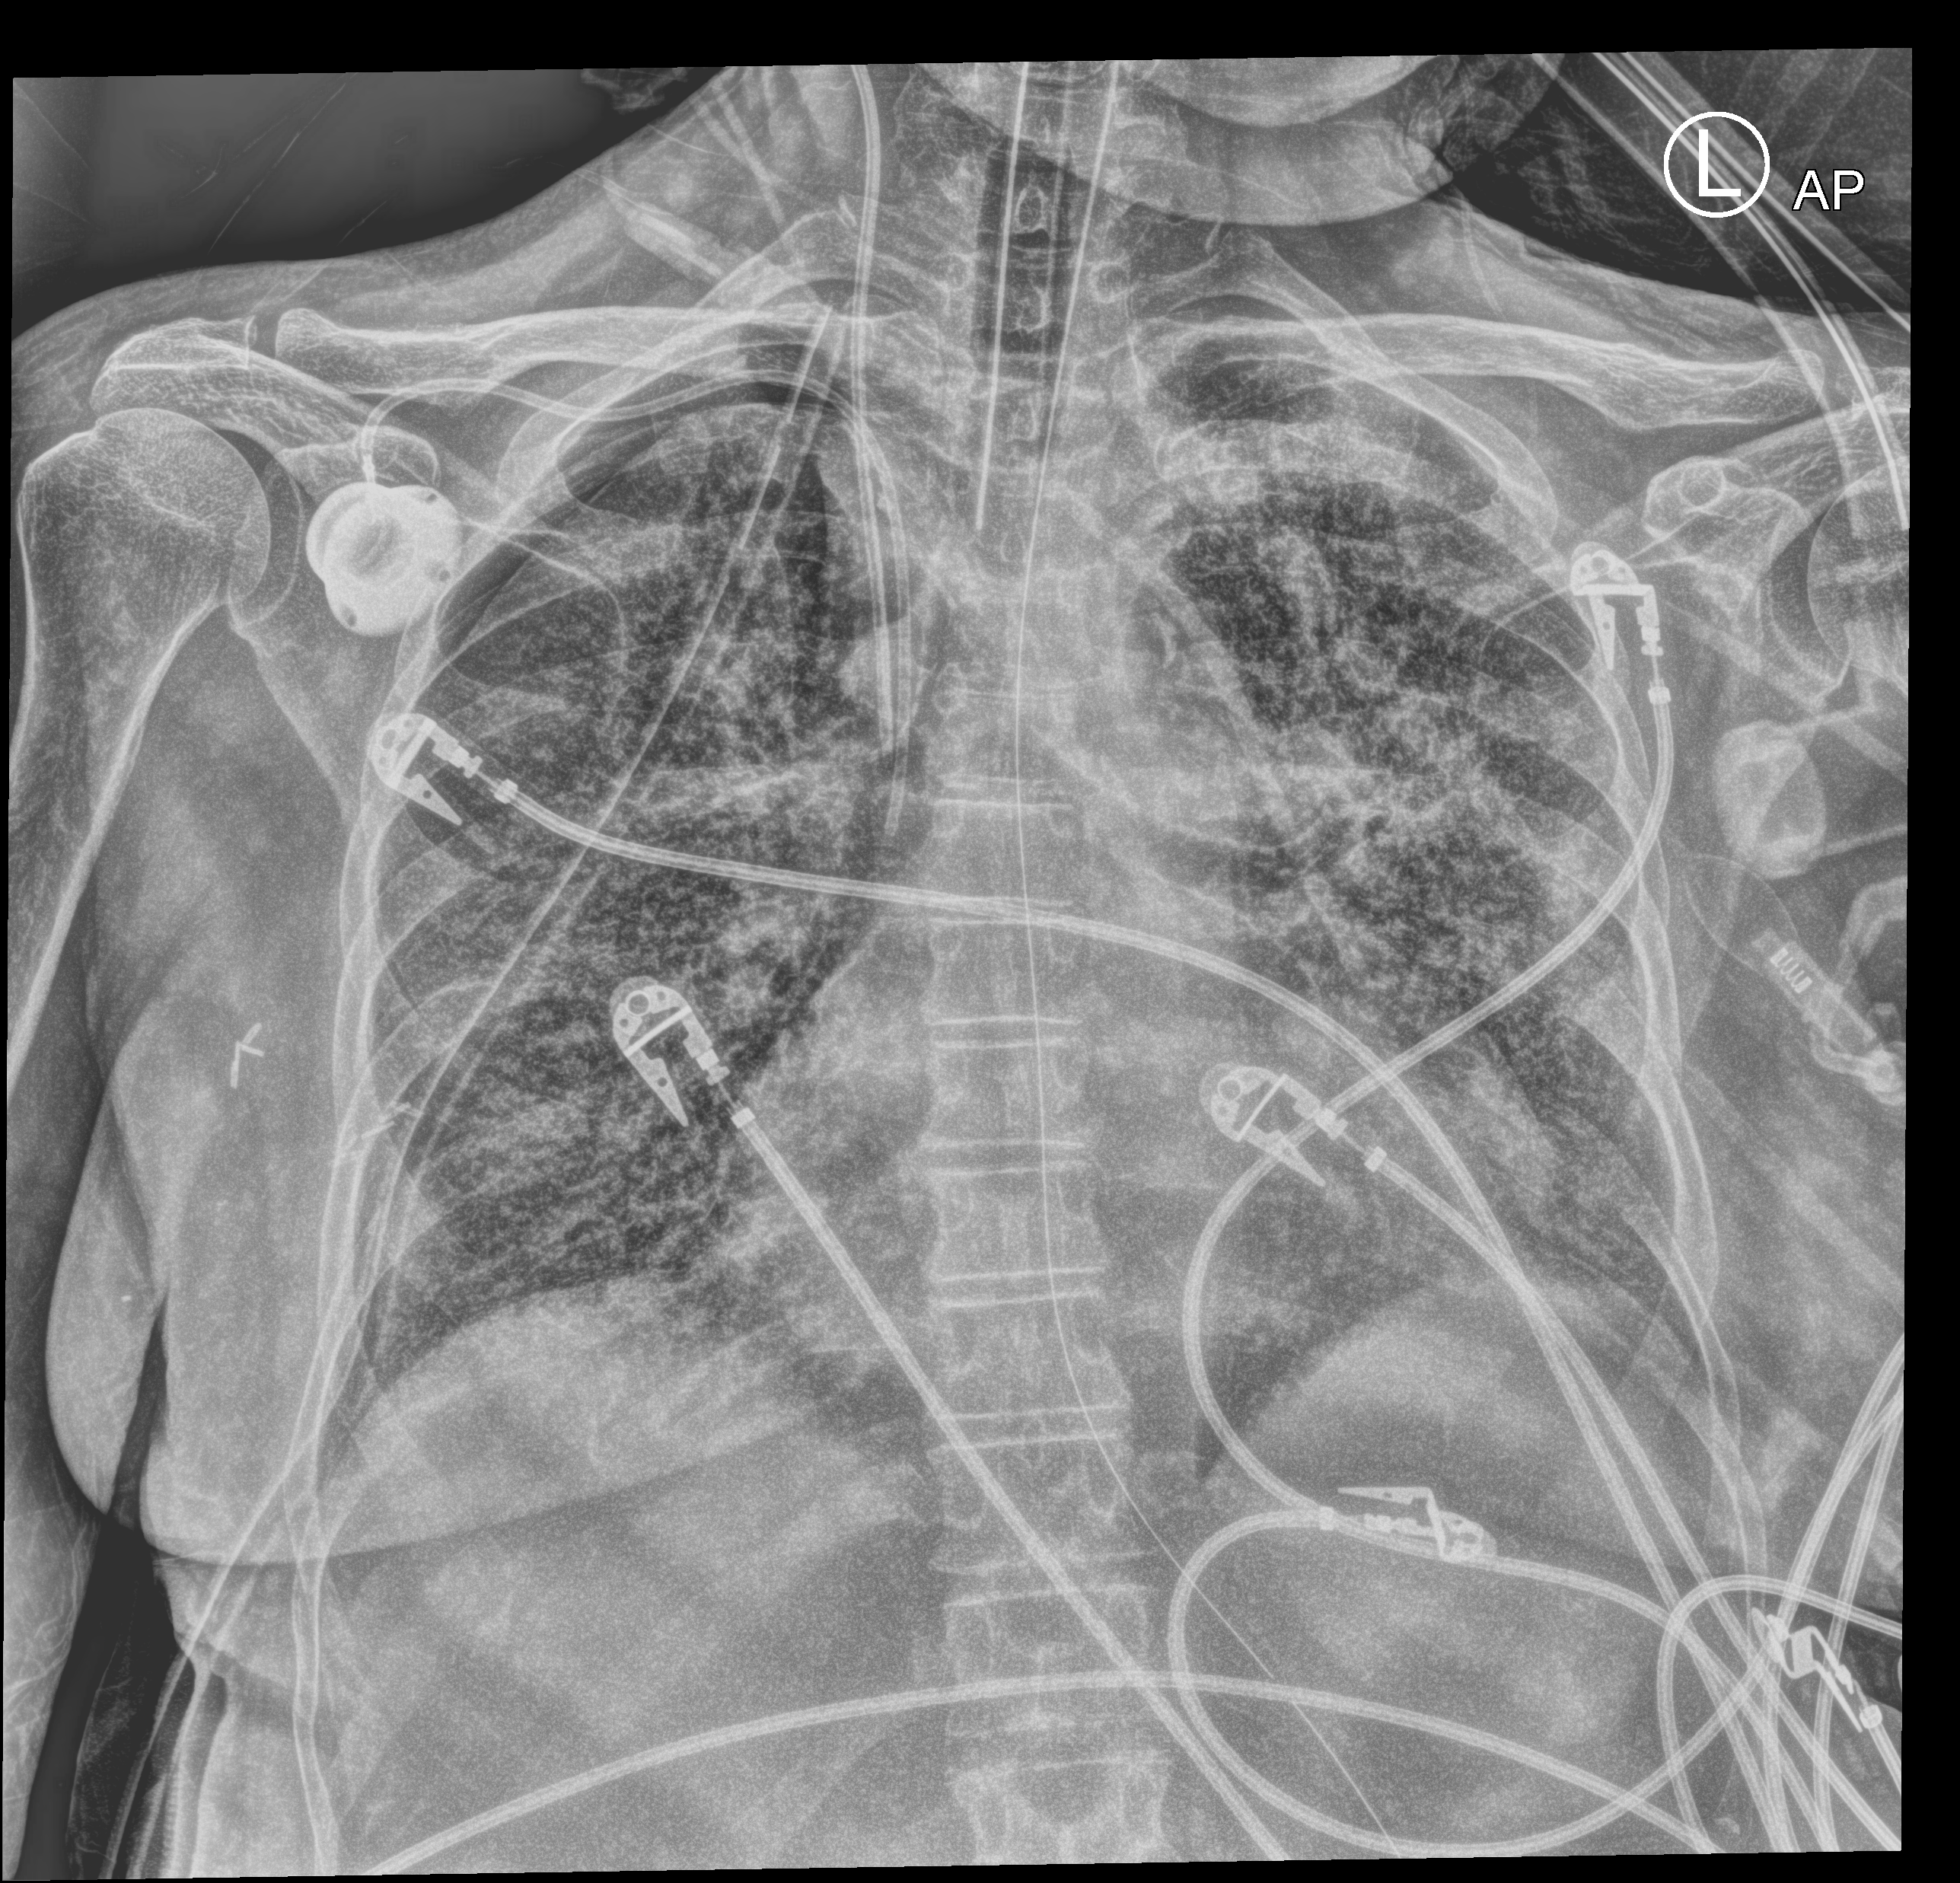
Chest X-ray (portable). Patient hospitalised with COVID-19; female, aged 60–74 years.
From the hospital-stay record, not from the radiograph (when in the stay this image was taken is not recorded): admitted to intensive care during this hospital stay: yes; length of hospital stay: 43 days.